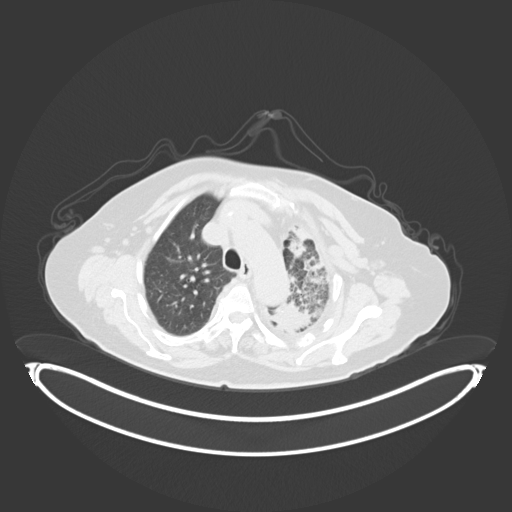
Chest CT, one axial slice. Position 220 of 284 along the scan axis. Reconstruction kernel B30f. 120 kVp. Lung window (W 1500 / L -600 HU). 512 × 512 image matrix. Patient: female, 75 years. From the clinical record (not read from this slice): clinical TNM (as recorded): T3 N3 M1.
Annotated regions visible in this slice (bounding box drawn by a radiologist):
- lung tumour (recorded histology: adenocarcinoma): box from (x=273, y=295) to (x=322, y=339) px